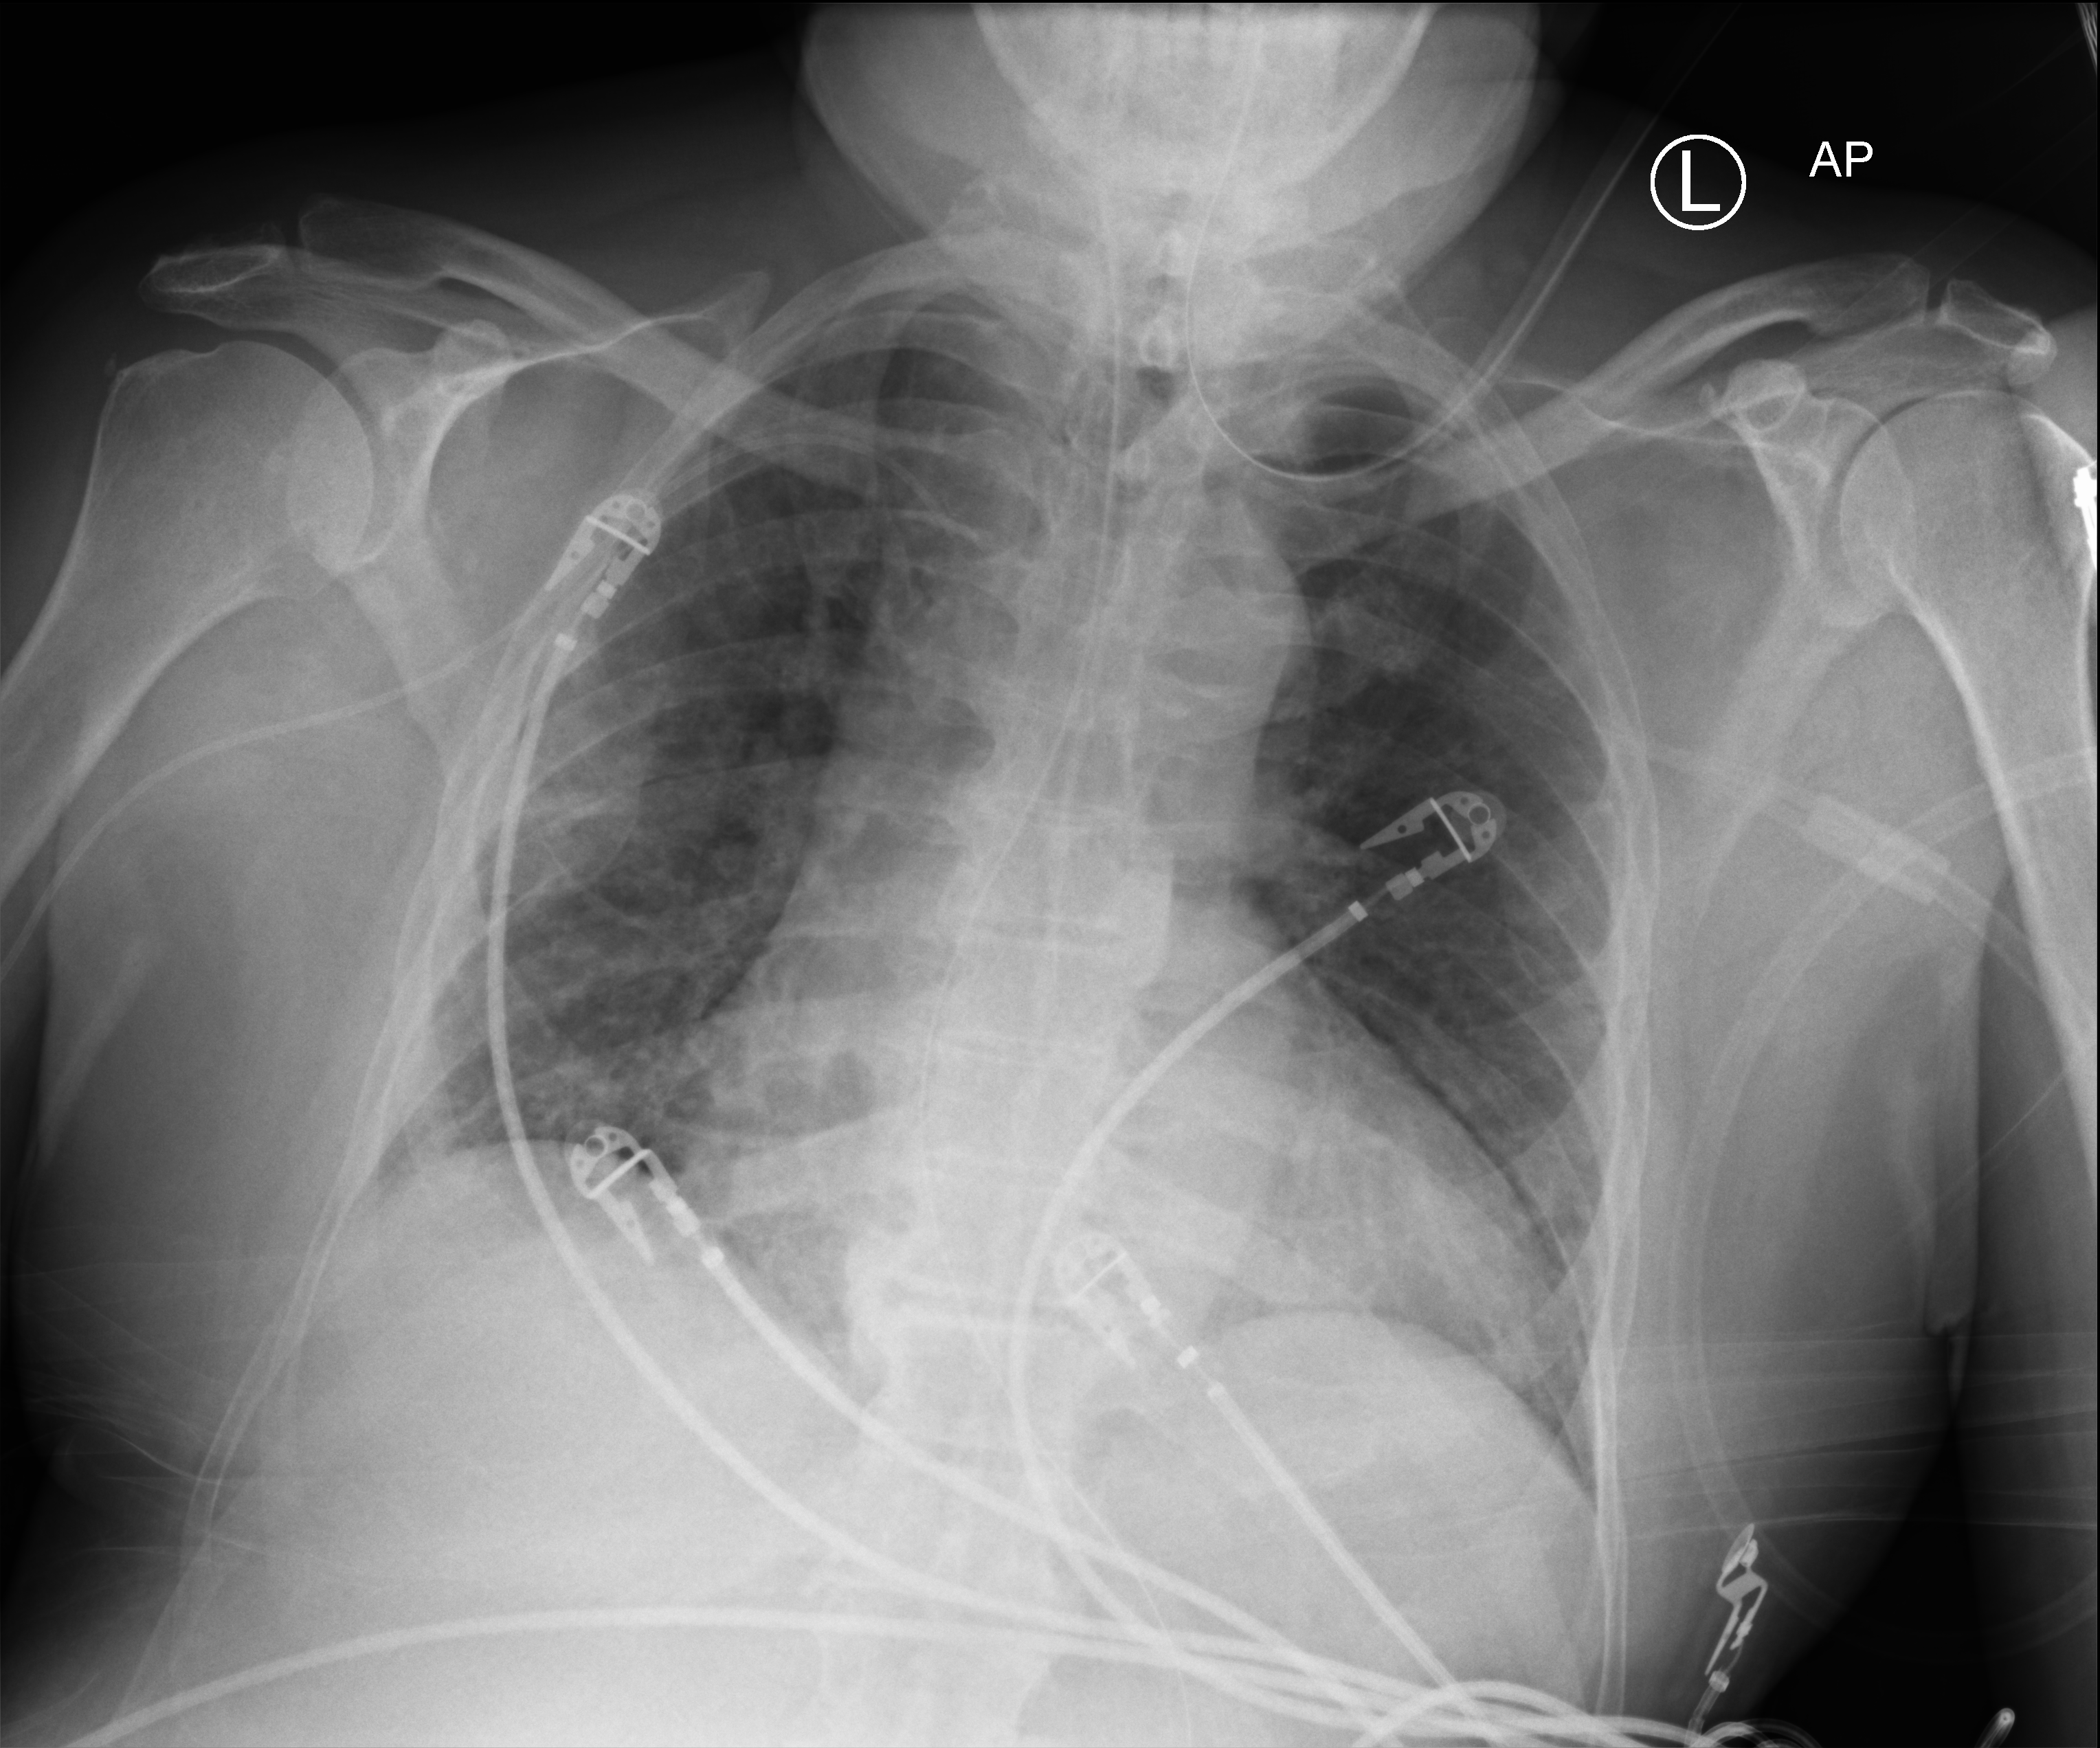
Chest X-ray (portable), anteroposterior (AP) projection. Male patient hospitalised with COVID-19, age 60–74 years.
Admission-level facts for this patient (not findings on this image; timing relative to this image not recorded):
- admitted to intensive care during this hospital stay: yes